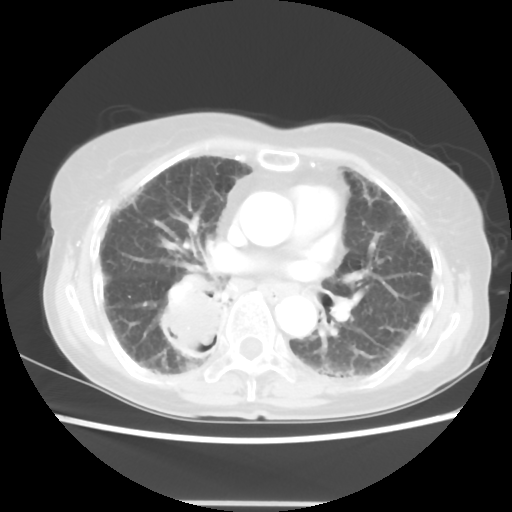
Chest CT, one axial slice. Reconstruction kernel STANDARD. 120 kVp. Lung window (W 1500 / L -600 HU). 5 mm slice thickness. 512 × 512 image matrix, field of view 325 × 325 mm. Patient: female, 71 years. From the clinical record (not read from this slice): clinical TNM (as recorded): T3 N0 M0.
Structures marked on this image (bounding box drawn by a radiologist):
- lung tumour (recorded histology: squamous cell carcinoma): box from (x=151, y=280) to (x=234, y=368) px